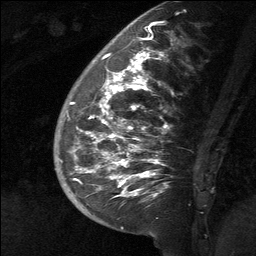
Breast MRI (dynamic contrast-enhanced), one sagittal slice; position 22 of 64 along the scan axis; dynamic contrast-enhanced study with each time point stored as its own series, time point 2 of 3 at this slice position (early post-contrast, ordered by acquisition time); 1.5 T; TE 4.8 ms, TR 27 ms; 256 × 256 image matrix, field of view 180 × 180 mm. Female patient, age 39 years. Case-level facts recorded for this patient, not image findings: setting: breast cancer imaged before/during neoadjuvant chemotherapy; receptor status: HER2-positive.
Outlined on this slice (semi-automatically segmented with operator editing):
- analysis volume of interest (the breast-tissue region the enhancement analysis was run in; not a lesion): bounding box (x1, y1, x2, y2) in pixels: (58, 40, 173, 217)
- tumour enhancement mask (voxels above the 90 % enhancement threshold inside the analysis volume of interest): (69, 51, 163, 196)